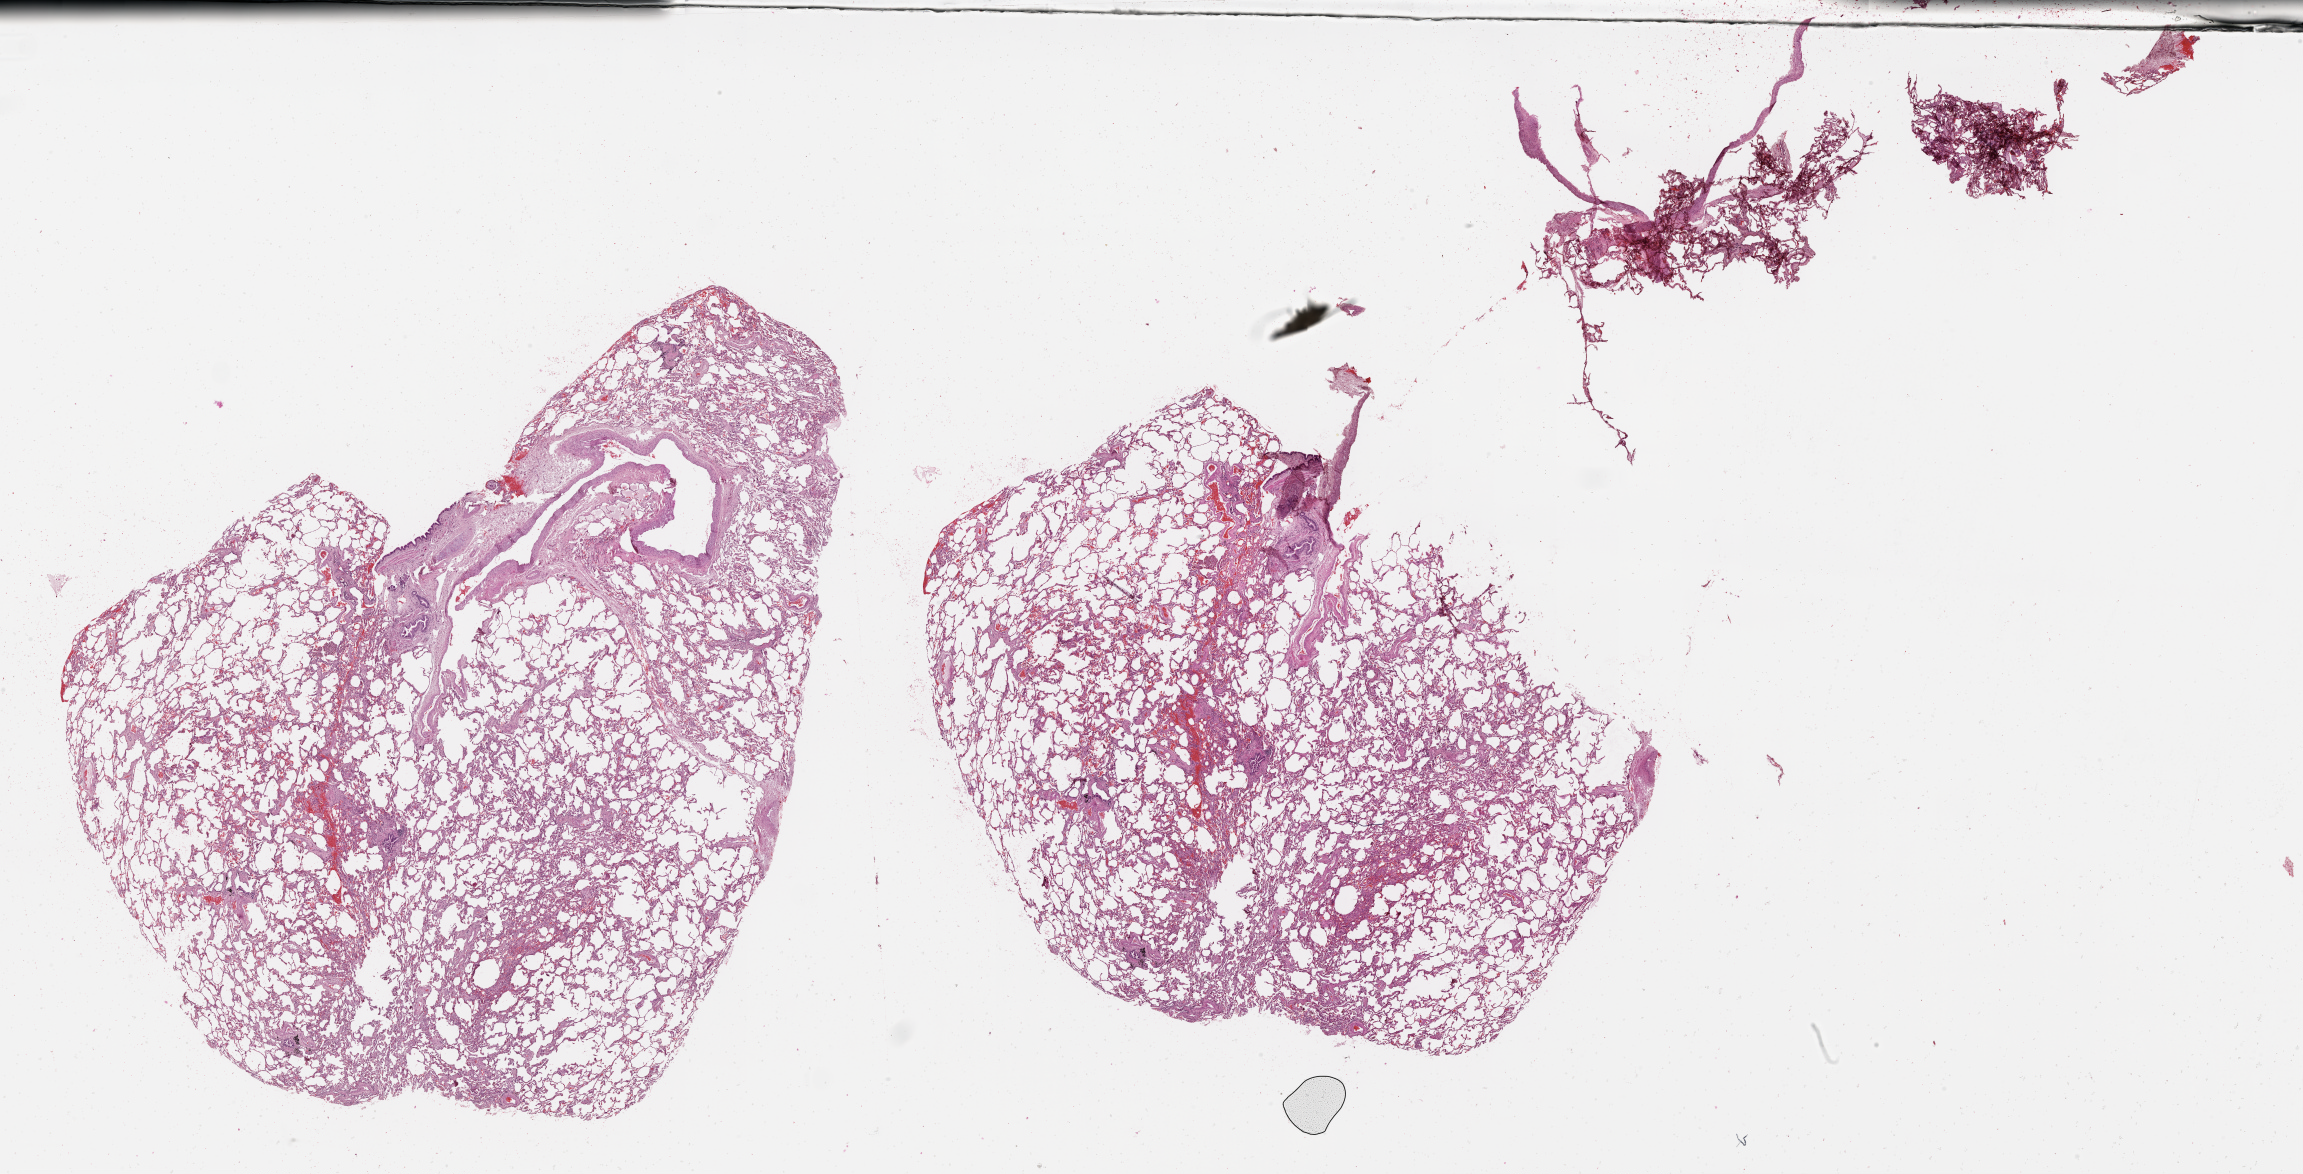
Whole-slide histology image, Hematoxylin and eosin (H&E) stained — shown as a low-resolution overview of the whole scanned area (about 37.1 x 18.9 mm, acquisition: 20x scan), lung, normal (non-tumour) tissue. 62-year-old female patient.
This section: normal (non-tumour) tissue from the same patient. Patient diagnosis (cohort enrolment): squamous cell carcinoma (lung).